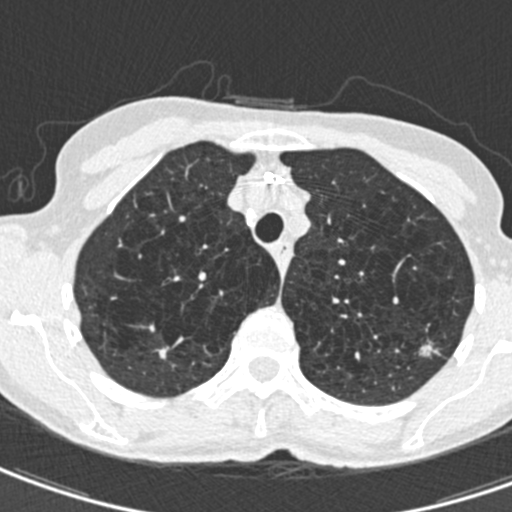
Chest CT (low-dose screening protocol), one axial image; second annual screen; lung window (W 1500 / L -600 HU); 0.75 mm slice thickness; 120 kVp; slice 118 of 498 in the series; 512 × 512 image matrix, field of view 272 × 272 mm. Female participant, aged 71 years at enrolment. Current smoker at enrolment.
• Expert-annotated lung lesion, box from (x=404, y=331) to (x=444, y=369) px.
• The screening reader recorded 2 non-calcified nodules or masses ≥4 mm on this exam (right upper lobe, left upper lobe); which of them this box marks is not recorded.
• Official screen result: positive, change unspecified: nodule(s) >= 4 mm or enlarging nodule(s), mass(es), or other non-specific abnormalities suspicious for lung cancer.
• Later outcome: lung cancer diagnosed 604 days after this screen (after the third annual screen) — adenocarcinoma, NOS, left upper lobe, moderately differentiated (G2), stage IA (AJCC 6th edition), 12 mm at pathology.